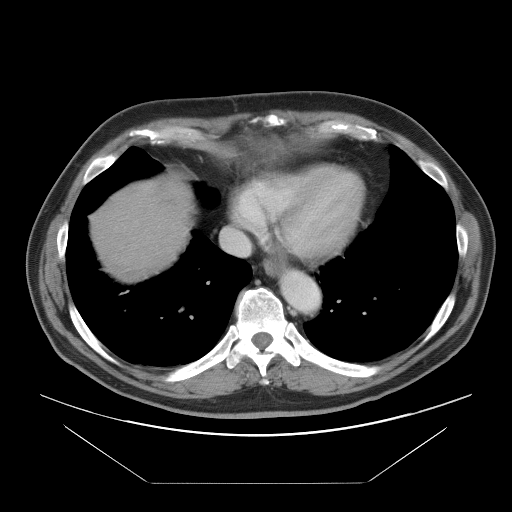
Contrast-enhanced abdominal CT, one axial slice. Position 87 of 97 along the scan axis. 120 kVp. Intravenous contrast given. Soft-tissue window (W 400 / L 40 HU). 5 mm slice thickness. 512 × 512 image matrix, field of view 442 × 442 mm. Male patient, age 62 years. Case-level facts recorded for this patient, not image findings: diagnosis: colorectal cancer liver metastases, imaged before liver resection; multiple liver metastases: no; largest metastasis: 7 cm; disease in both lobes: yes.
Structures marked on this image (outlined manually by an expert reader):
- hepatic veins: box from (x=221, y=191) to (x=264, y=256) px
- liver: (x=95, y=178)–(x=188, y=274)
- planned liver remnant (the part of the liver to remain after resection): (x=95, y=188)–(x=188, y=274)